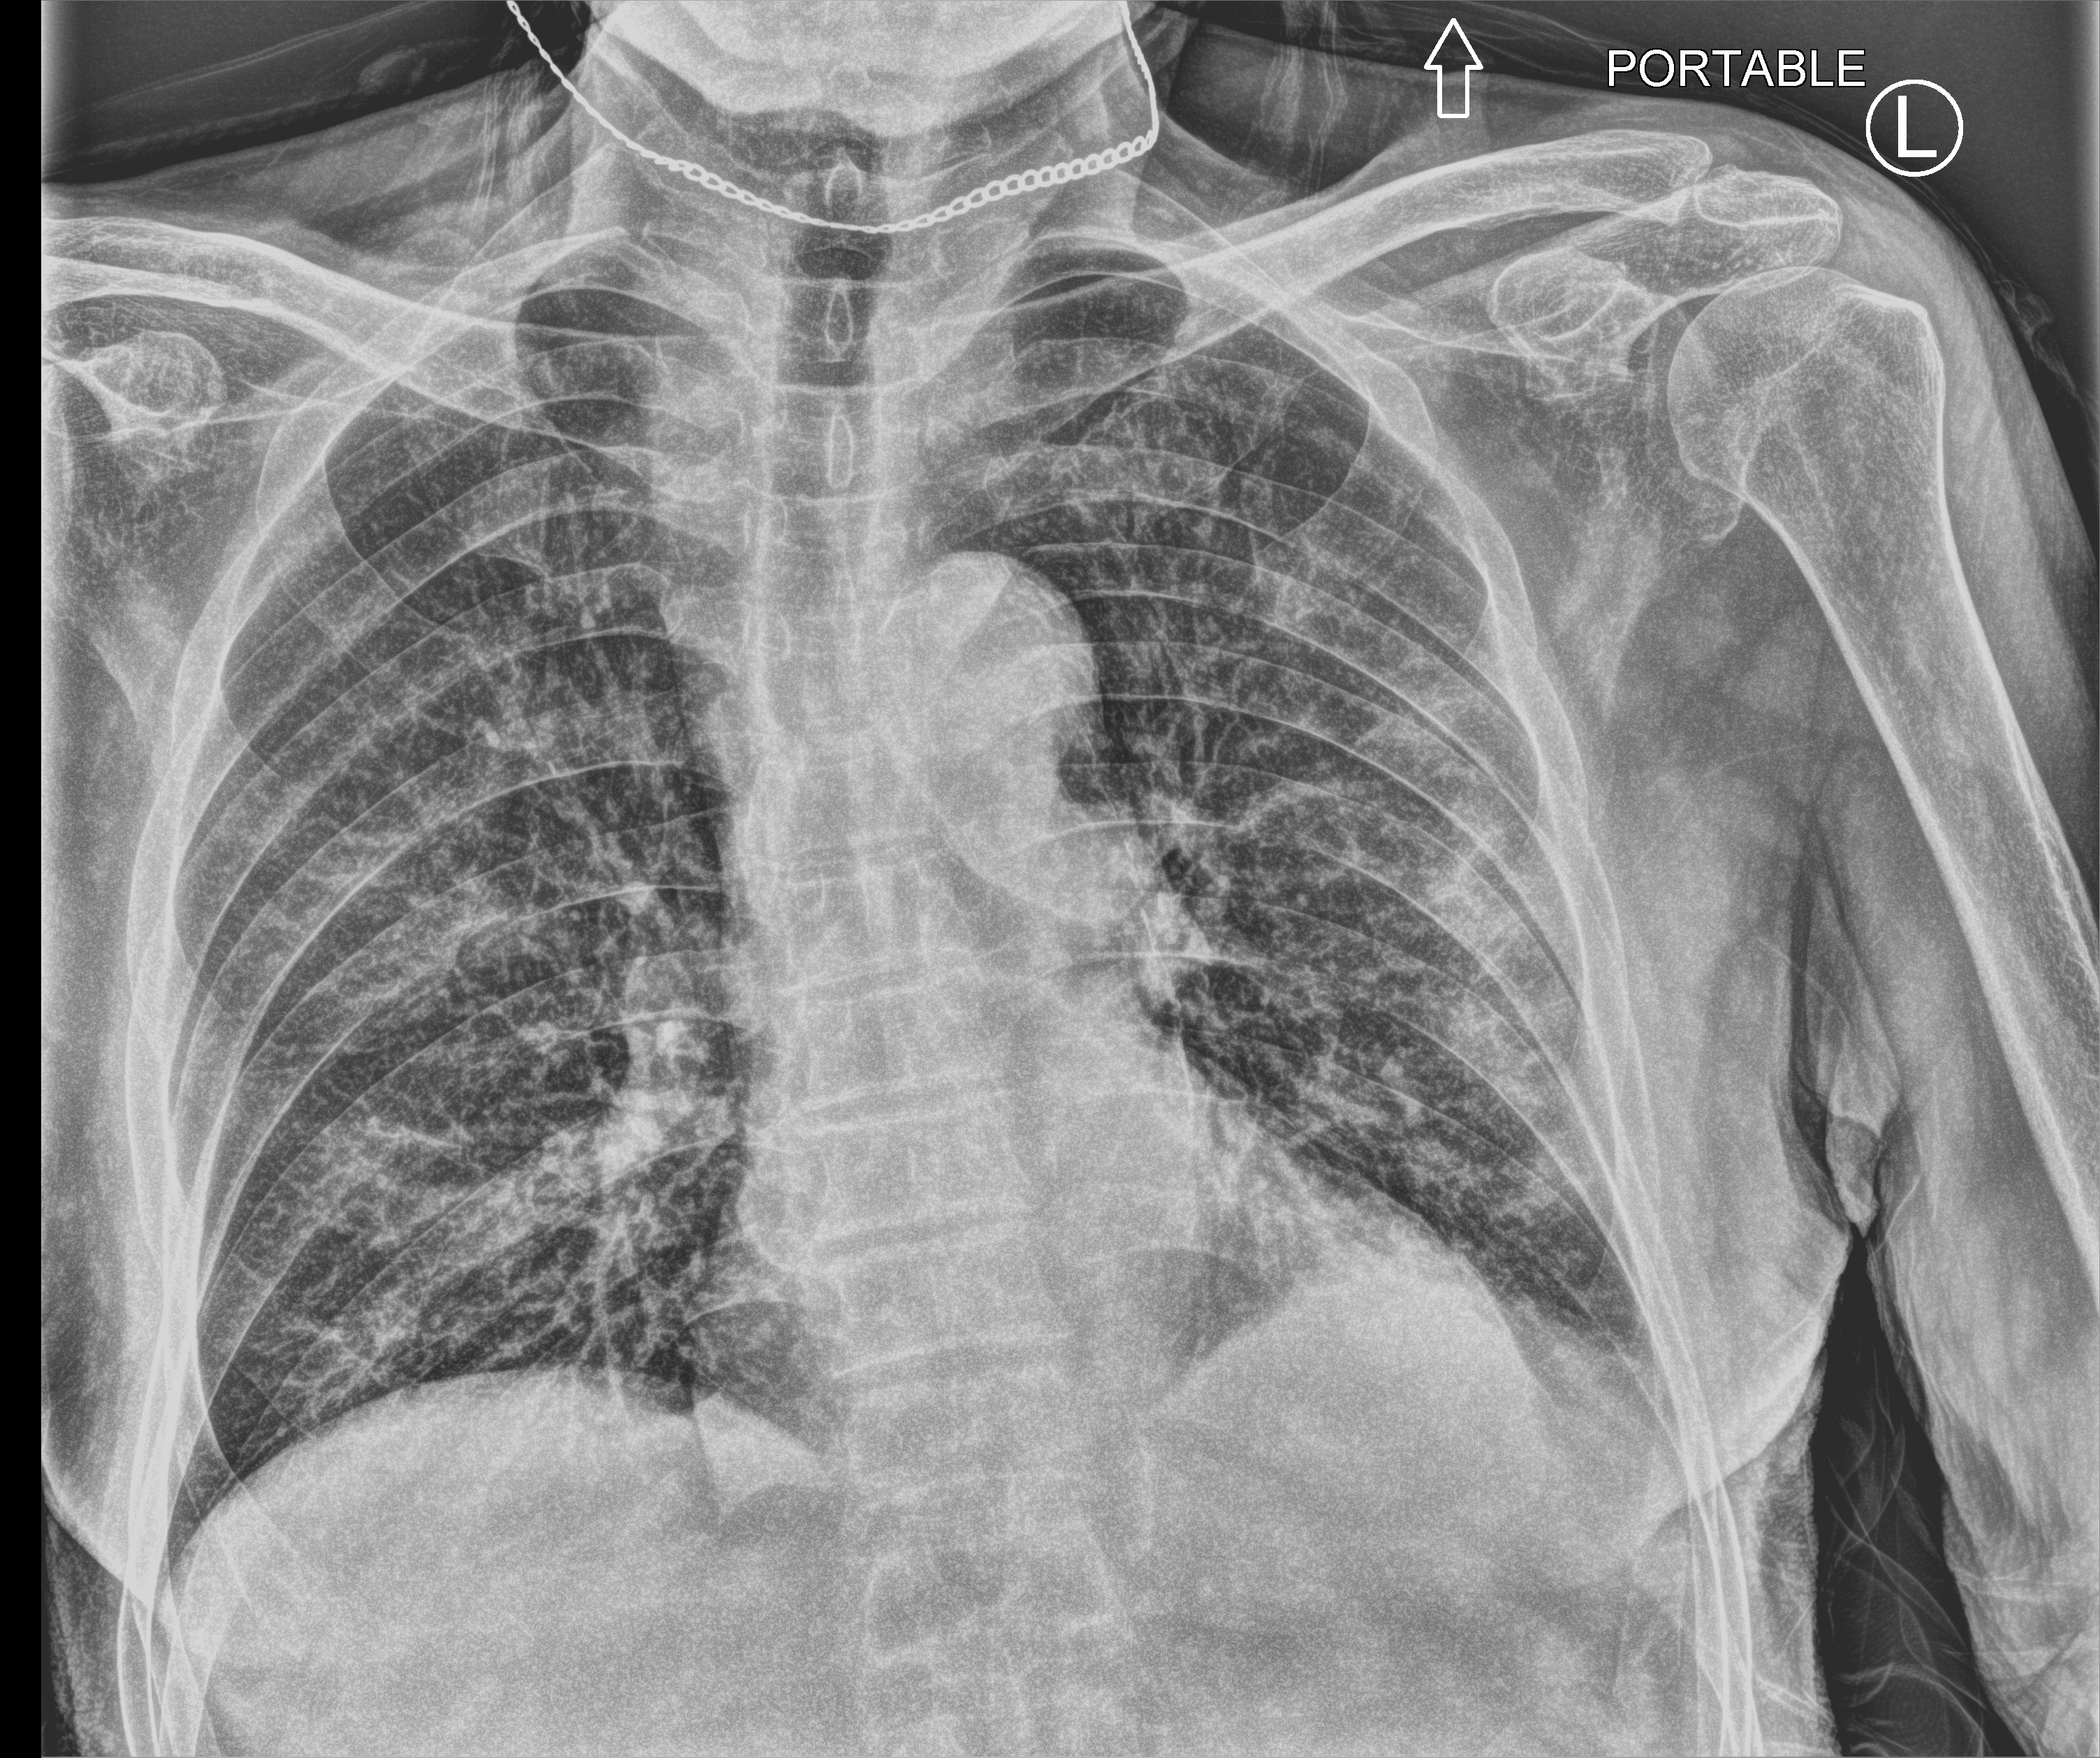
Bedside chest radiograph (computed radiography); anteroposterior (AP) projection. Male patient hospitalised with COVID-19, age 75–90 years.
Hospital-stay facts (about this admission, not read from this image; timing relative to this image not recorded): mechanically ventilated during this hospital stay: no; COPD (admission record): no; admitted to intensive care during this hospital stay: no.